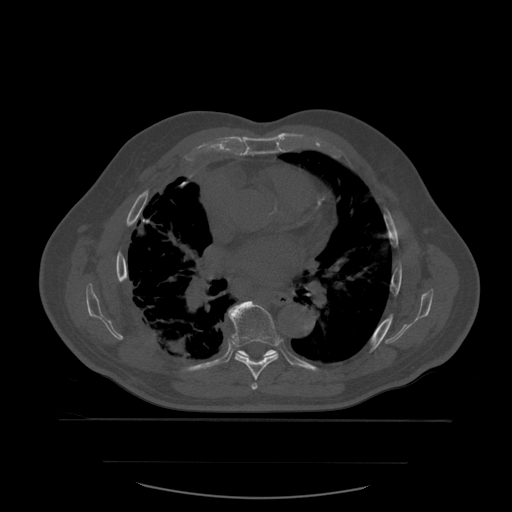
CT including the spine, one axial slice. Position 379 of 590 along the scan axis. Bone window (W 1800 / L 400 HU). 1.25 mm slice thickness. 512 × 512 image matrix, field of view 479 × 479 mm. Patient age 71 years. From the clinical record (not read from this slice): primary cancer: lung; vertebrae with lytic lesions (as recorded): T1, T2, L5, S1.
Structures marked on this image (semi-automatically segmented with operator editing):
- T6 vertebra: bounding box [x1, y1, x2, y2] px = [252, 383, 258, 390]
- T7 vertebra: [228, 301, 279, 381]
- T8 vertebra: [238, 350, 276, 359]